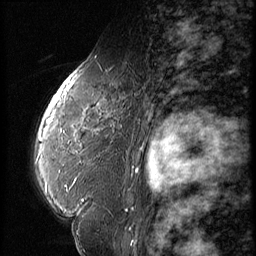
Breast MRI (dynamic contrast-enhanced), one sagittal slice; slice 38 of 56 in the series (ordered by position); dynamic contrast-enhanced series, image 2 of 3 at this slice position (ordered by acquisition); 1.5 T; TE 4.2 ms, TR 9 ms; 2.5 mm slice thickness; 256 × 256 image matrix. Patient: female, 59 years. From the clinical record (not read from this slice): setting: breast cancer imaged before/during neoadjuvant chemotherapy; receptor status: HER2-positive.
Structures marked on this image (semi-automatically segmented with operator editing):
- analysis volume of interest (the breast-tissue region the enhancement analysis was run in; not a lesion): bounding box <44,66,151,135> (left, top, right, bottom; pixels)
- tumour enhancement mask (voxels above the 140 % enhancement threshold inside the analysis volume of interest): <45,82,69,117>